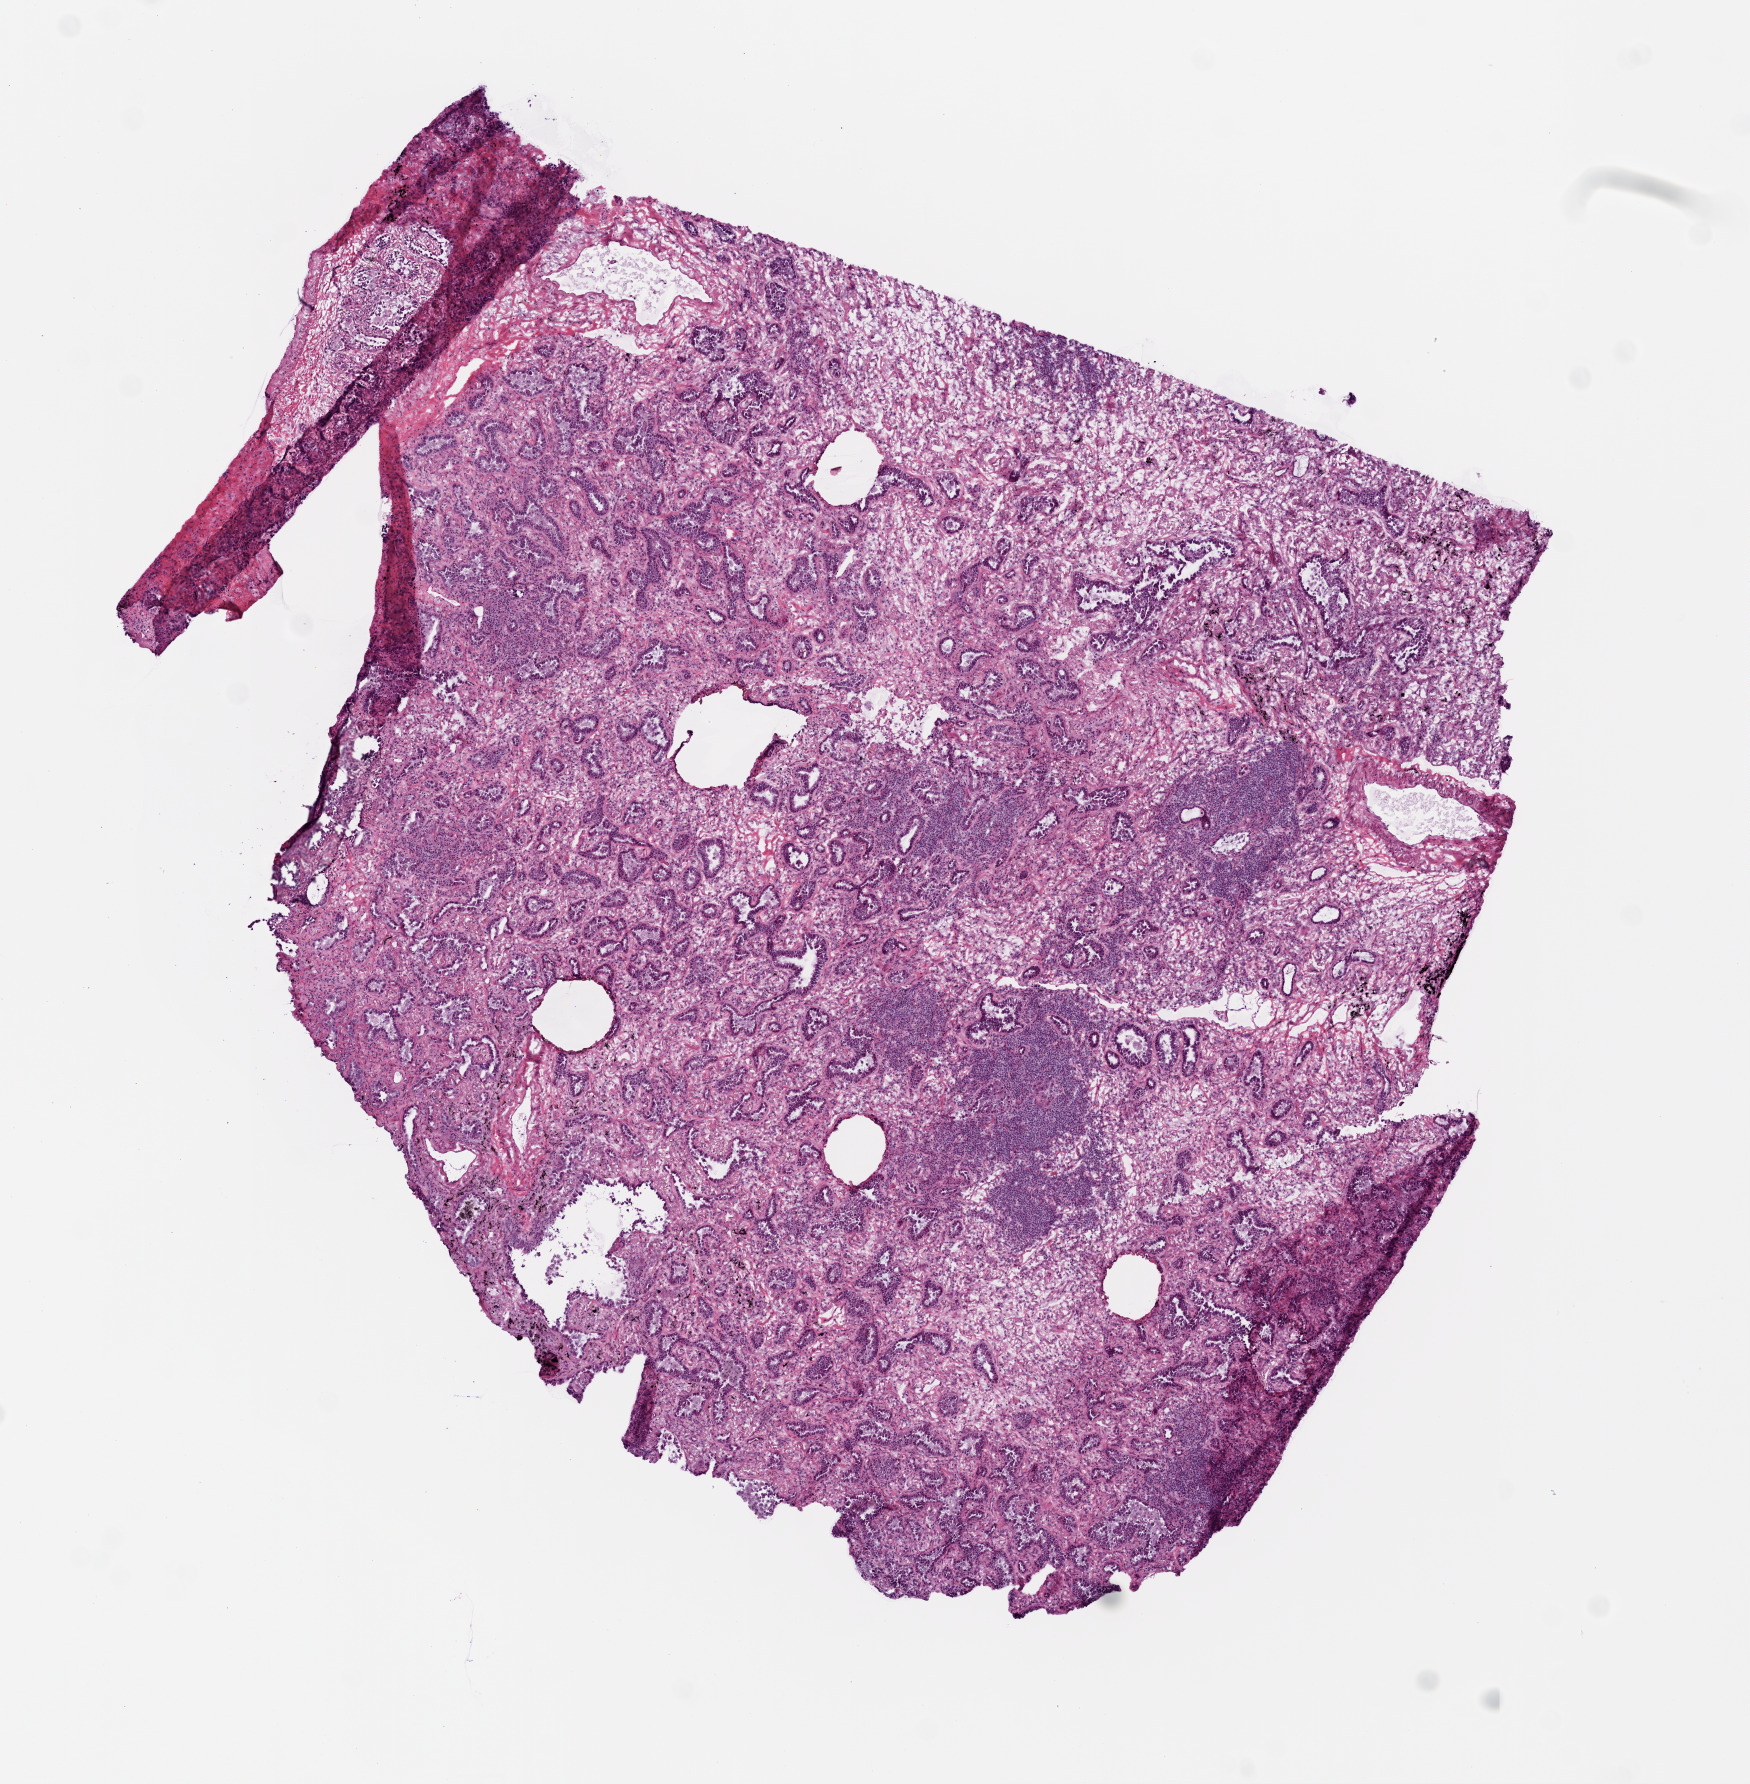
Hematoxylin and eosin (H&E) stained whole-slide image, low-resolution overview of the scanned area, about 7.0 x 7.2 mm (acquisition: 20x scan); frozen section from the top of the tissue portion; lung, primary tumour sample. Female, age 75 years at initial diagnosis. Composition of this section per pathologist review: tumour cells 100%, tumour nuclei 70%, normal cells 0%, stromal cells 0%, necrosis 0%. Infiltration values recorded for this section: lymphocyte infiltration 20%, monocyte infiltration 0%, neutrophil infiltration 0%.
* laterality: right
* AJCC pathologic stage: IB
* diagnosis: Acinar cell carcinoma (upper lobe, lung)